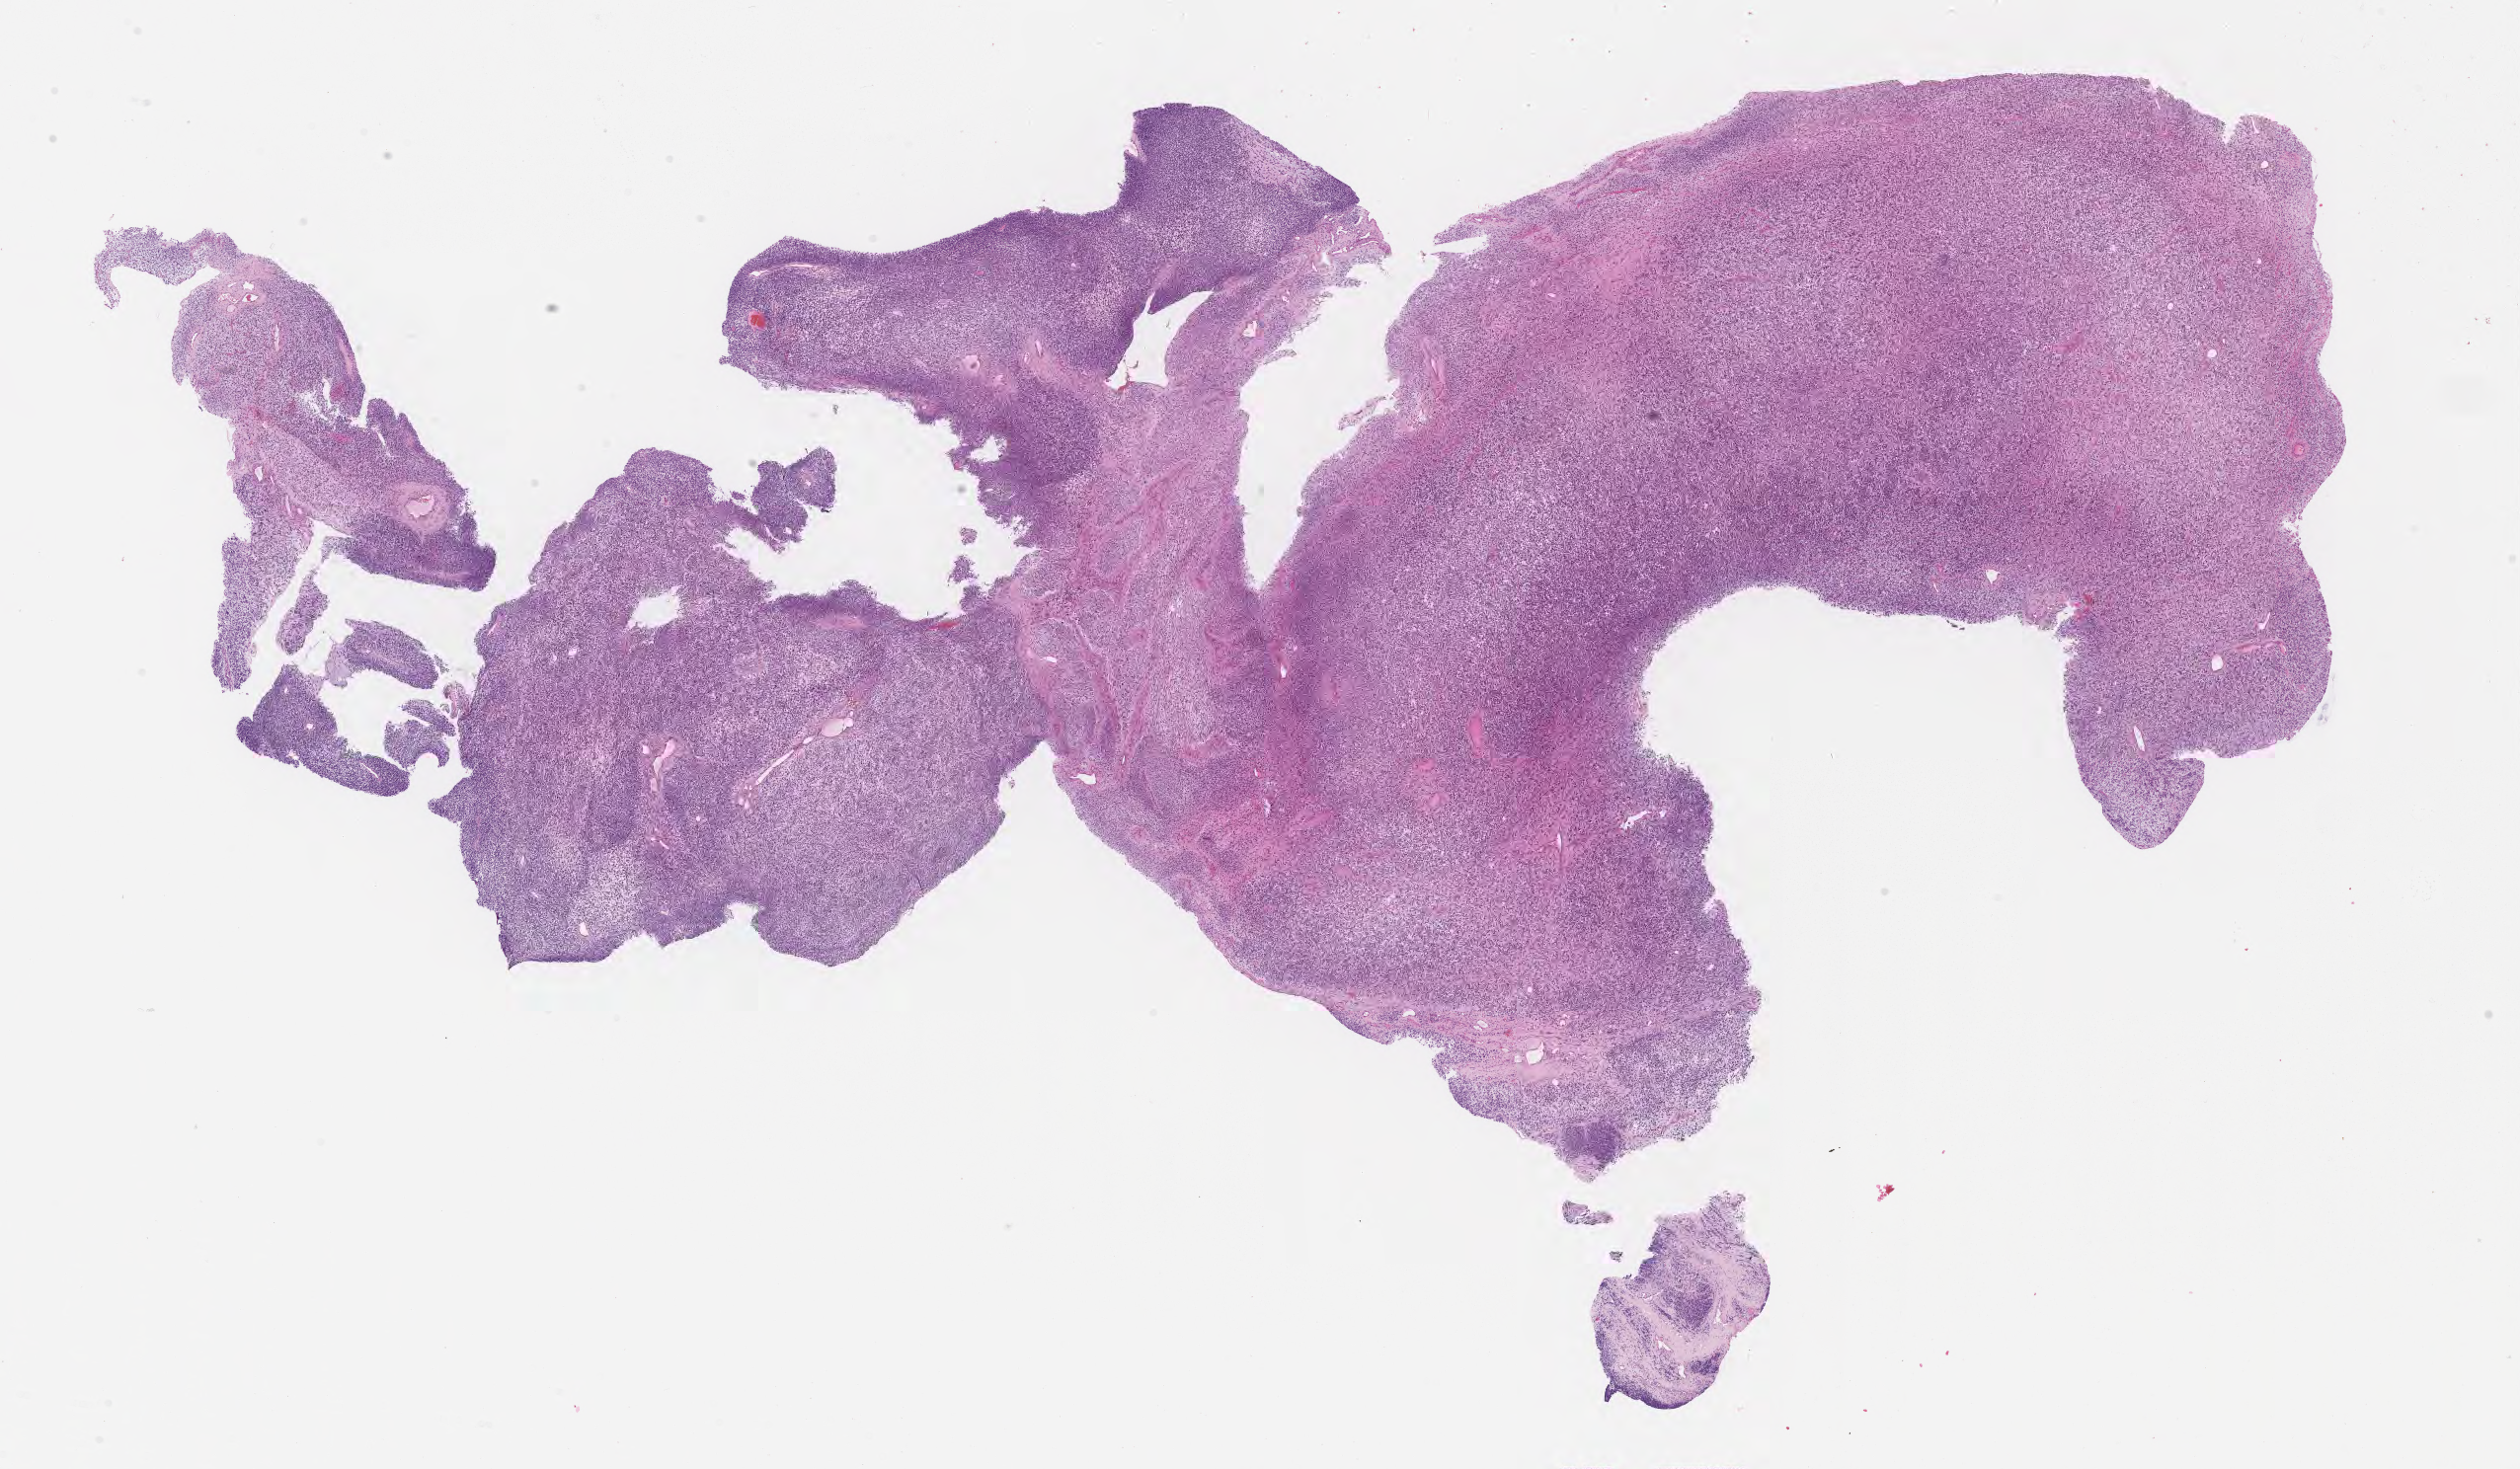
Digitized haematoxylin and eosin-stained section of tumor tissue, low-resolution overview of the scanned area, about 20.6 x 12.0 mm; FFPE section; sample anatomic site: soft tissue, pelvis-left. Patient: male, age 4.3 years at diagnosis.
Diagnosis: rhabdomyosarcoma; histological classification: embryonal rhabdomyosarcoma. Metastatic status at presentation (as recorded): non-metastatic (unconfirmed). Primary site (case record): pelvis, site indeterminate. Stage (as recorded): 3.